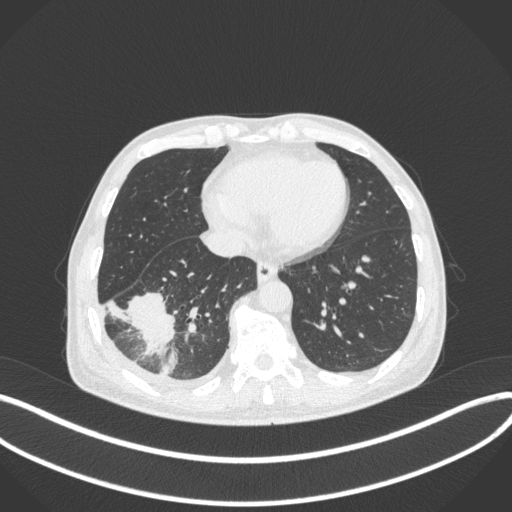
Chest CT, one axial slice; slice 117 of 385 in the series (ordered by position); reconstruction kernel B31f; 120 kVp; lung window (W 1500 / L -600 HU); 512 × 512 image matrix, field of view 400 × 400 mm. Patient: male, 64 years. Case-level facts recorded for this patient, not image findings: clinical TNM (as recorded): T3 N0 M0; histopathological grade: G2-3.
Annotated regions visible in this slice (bounding box drawn by a radiologist):
- lung tumour (recorded histology: adenocarcinoma): bounding box [x1, y1, x2, y2] px = [126, 283, 176, 357]